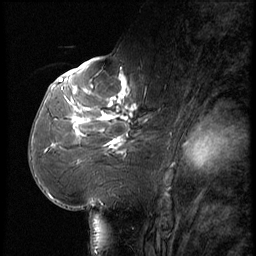
Breast MRI (dynamic contrast-enhanced), one sagittal slice. Position 31 of 56 along the scan axis. Dynamic contrast-enhanced series, image 2 of 3 at this slice position (ordered by acquisition). 1.5 T. TE 4.2 ms, TR 9 ms. 2.5 mm slice thickness. 256 × 256 image matrix. Female patient, age 61 years. Case-level facts recorded for this patient, not image findings: setting: breast cancer imaged before/during neoadjuvant chemotherapy; receptor status: HR-positive, HER2-negative.
Structures marked on this image (semi-automatically segmented with operator editing):
- analysis volume of interest (the breast-tissue region the enhancement analysis was run in; not a lesion): bounding box [x1, y1, x2, y2] px = [65, 74, 160, 175]
- tumour enhancement mask (voxels above the 140 % enhancement threshold inside the analysis volume of interest): [72, 74, 136, 150]